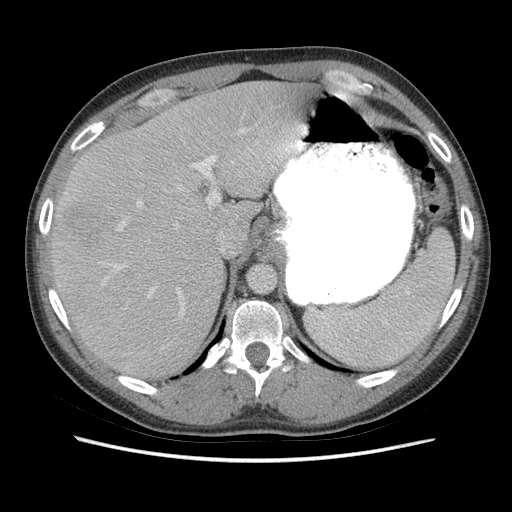
Contrast-enhanced abdominal CT (liver protocol), one axial slice; reconstruction kernel STANDARD; soft-tissue window (W 400 / L 40 HU); 512 × 512 image matrix, field of view 360 × 360 mm. From the clinical record (not read from this slice): diagnosis: hepatocellular carcinoma (patient treated with transarterial chemoembolisation; whether this scan precedes or follows treatment is not stated here); TNM stage (as recorded): Stage-IIIA; Child-Pugh class: A; tumour size: 6.6 cm.
Structures marked on this image (semi-automatic segmentation, software-assisted and operator-edited):
- liver parenchyma outside the tumour (the mass and vessels are separate outlines, so this box may not span the whole liver): box from (x=50, y=81) to (x=308, y=378) px
- mass: (x=58, y=200)–(x=105, y=257)
- liver vessels: (x=101, y=124)–(x=307, y=315)